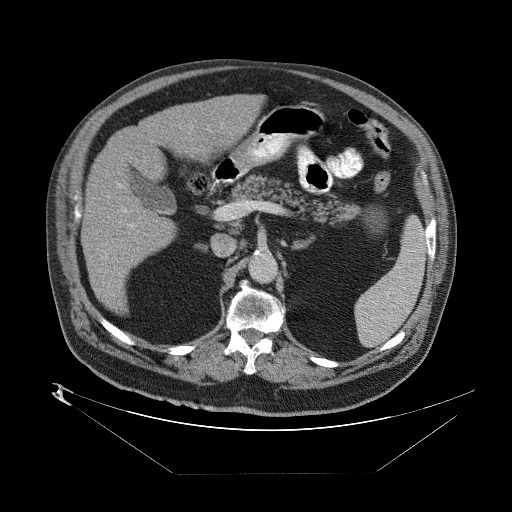
Contrast-enhanced abdominal CT (liver protocol), one axial slice; position 37 of 89 along the scan axis; 140 kVp; one of 2 acquisitions stored at this slice position; soft-tissue window (W 400 / L 40 HU); 2.5 mm slice thickness; 512 × 512 image matrix, field of view 480 × 480 mm. Case-level facts recorded for this patient, not image findings: diagnosis: hepatocellular carcinoma (patient treated with transarterial chemoembolisation; whether this scan precedes or follows treatment is not stated here); TNM stage (as recorded): Stage-II; Child-Pugh class: B; tumour size: 4 cm.
Annotated regions visible in this slice (semi-automatically segmented with operator editing):
- abdominal aorta: bounding box (x1, y1, x2, y2) in pixels: (250, 255, 275, 281)
- liver parenchyma outside the tumour (the mass and vessels are separate outlines, so this box may not span the whole liver): (82, 92, 264, 316)
- liver vessels: (94, 121, 224, 284)